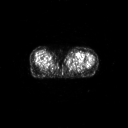
FDG PET of an extremity soft-tissue mass (from a PET/CT study), one axial slice. Slice 53 of 91 in the series (ordered by position). 3.27 mm slice thickness. 128 × 128 image matrix. Female patient, age 74 years. From the clinical record (not read from this slice): histological type: pleomorphic leiomyosarcoma; grade: high; site of the primary tumour: left thigh.
Structures marked on this image (expert contour drawn on MRI and transferred to this co-registered scan by the dataset authors):
- gross tumour volume including surrounding oedema: bounding box (x1, y1, x2, y2) in pixels: (67, 54, 76, 59)